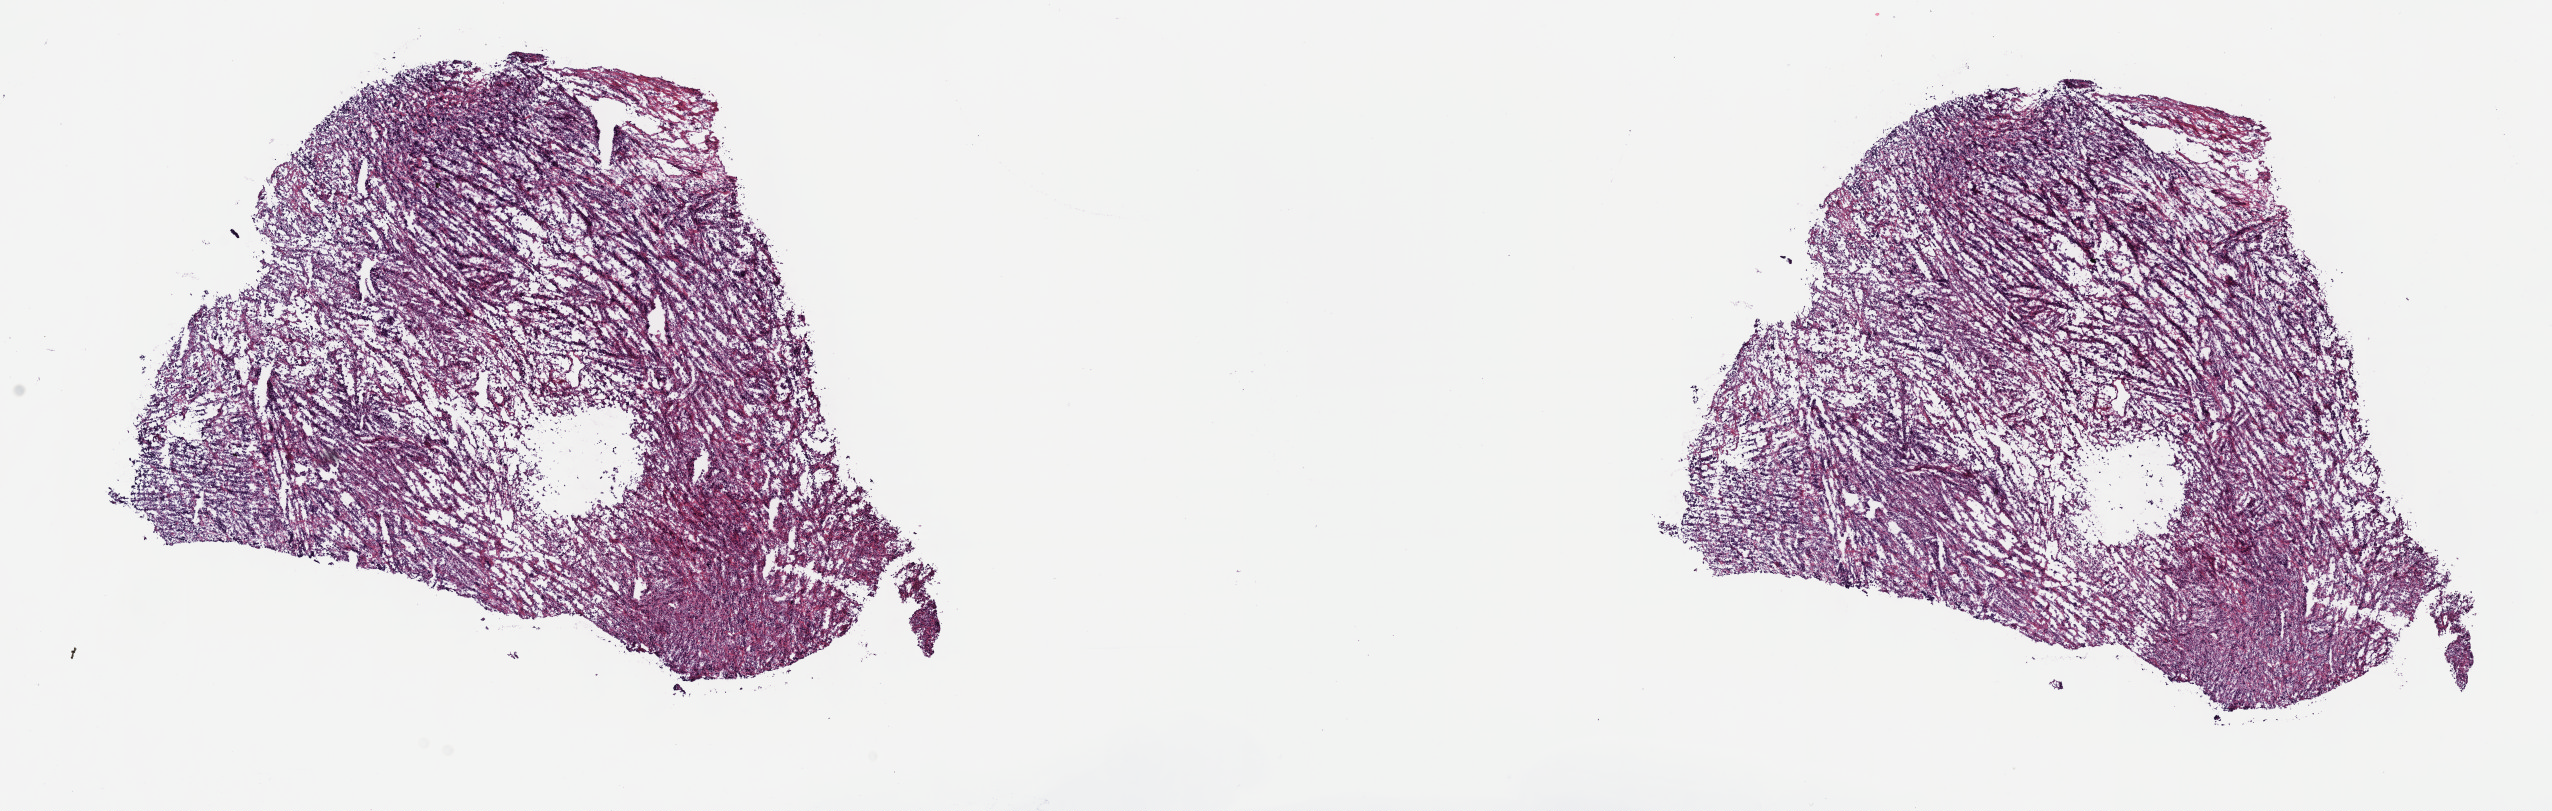
Whole-slide histology image, H&E — low-resolution overview of the scanned area, about 20.6 x 6.6 mm; frozen section from the top of the tissue portion; testis, primary tumour sample. Male, age 36 years at initial diagnosis. Slide review estimates, as recorded: tumour cells 100%, tumour nuclei 80%.
Pathologic diagnosis: Seminoma, NOS.